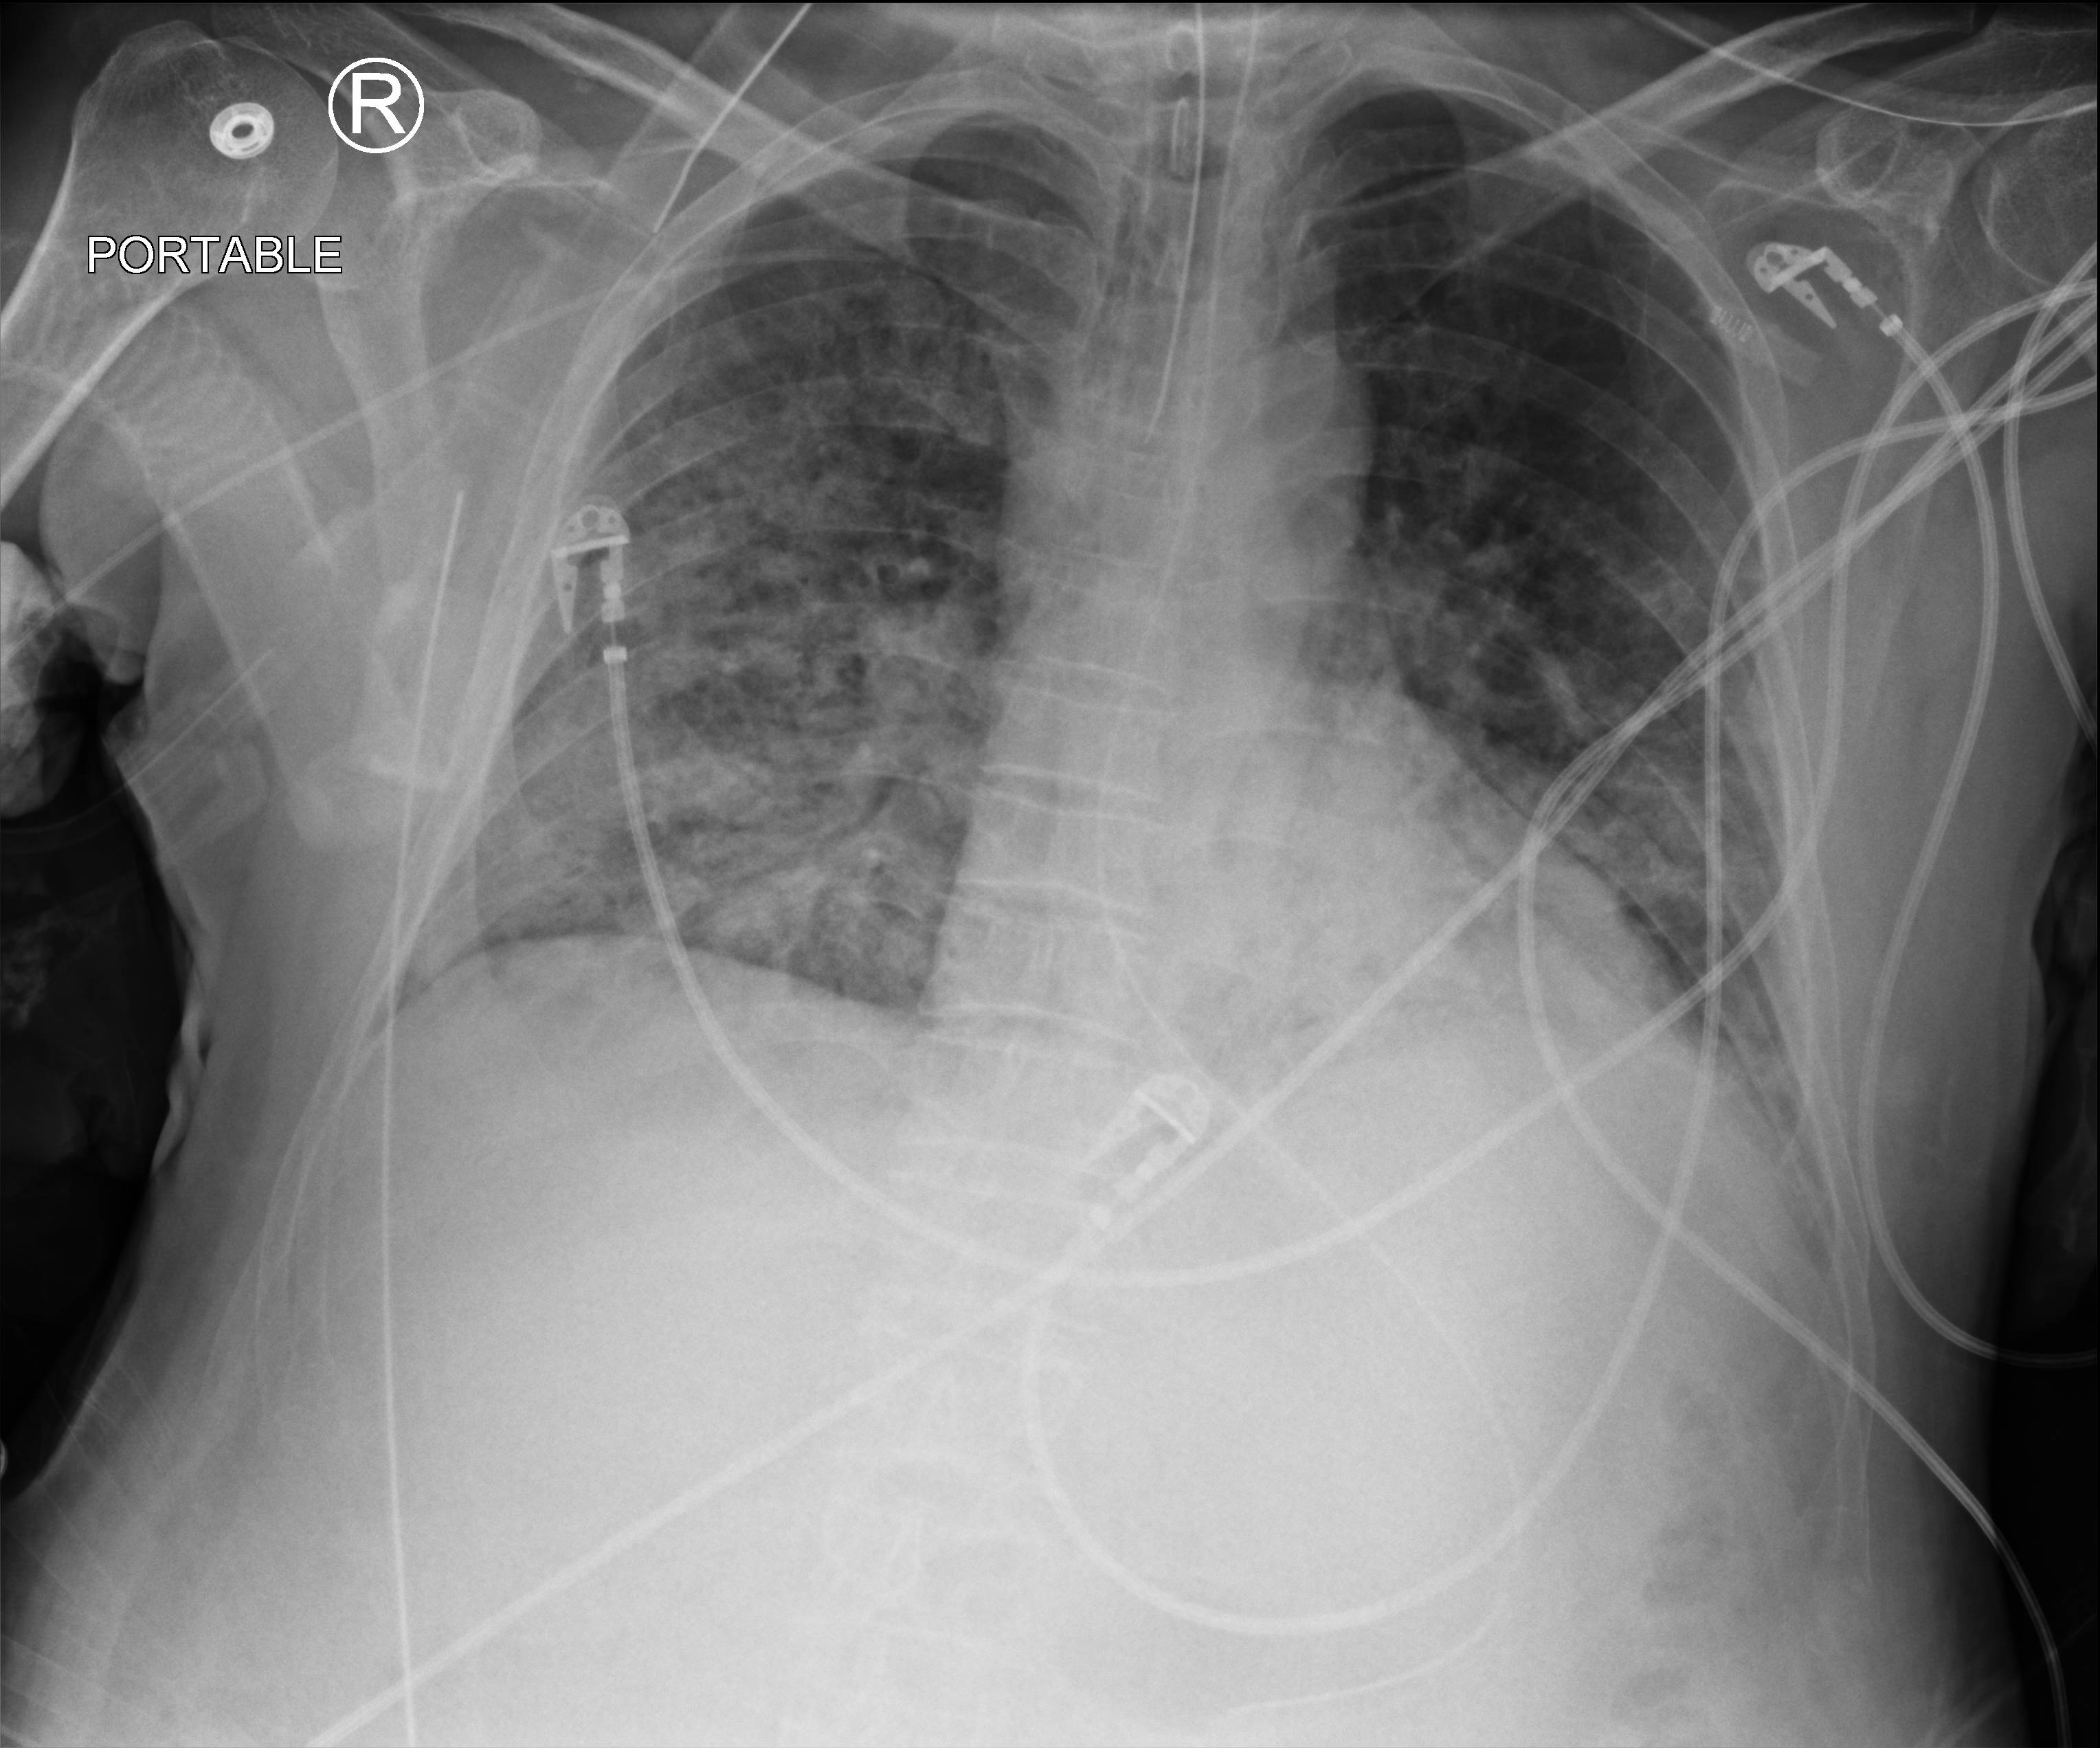
Chest X-ray (portable), anteroposterior (AP) projection. Male patient hospitalised with COVID-19, age 60–74 years.
Admission-level facts for this patient (not findings on this image; timing relative to this image not recorded): length of hospital stay: 19 days; mechanically ventilated during this hospital stay: yes; admitted to intensive care during this hospital stay: yes.